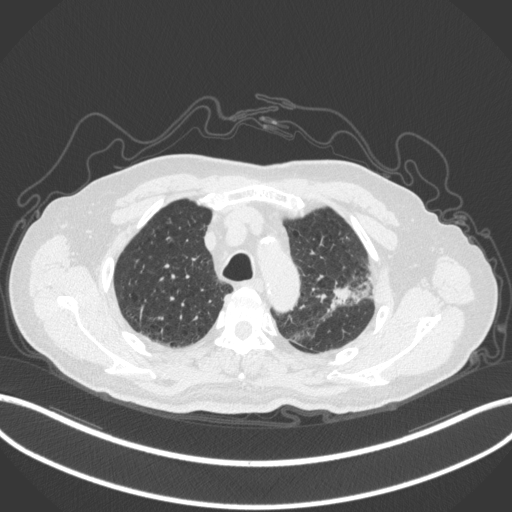
Chest CT, one axial slice; slice 238 of 331 in the series (ordered by position); reconstruction kernel B31f; 120 kVp; lung window (W 1500 / L -600 HU); 1 mm slice thickness; 512 × 512 image matrix. Male patient, age 79 years. From the clinical record (not read from this slice): clinical TNM (as recorded): T2a N1 M1; histopathological grade: G3.
Structures marked on this image (bounding box drawn by a radiologist):
- lung tumour (recorded histology: adenocarcinoma): bounding box (x1, y1, x2, y2) in pixels: (324, 284, 372, 311)